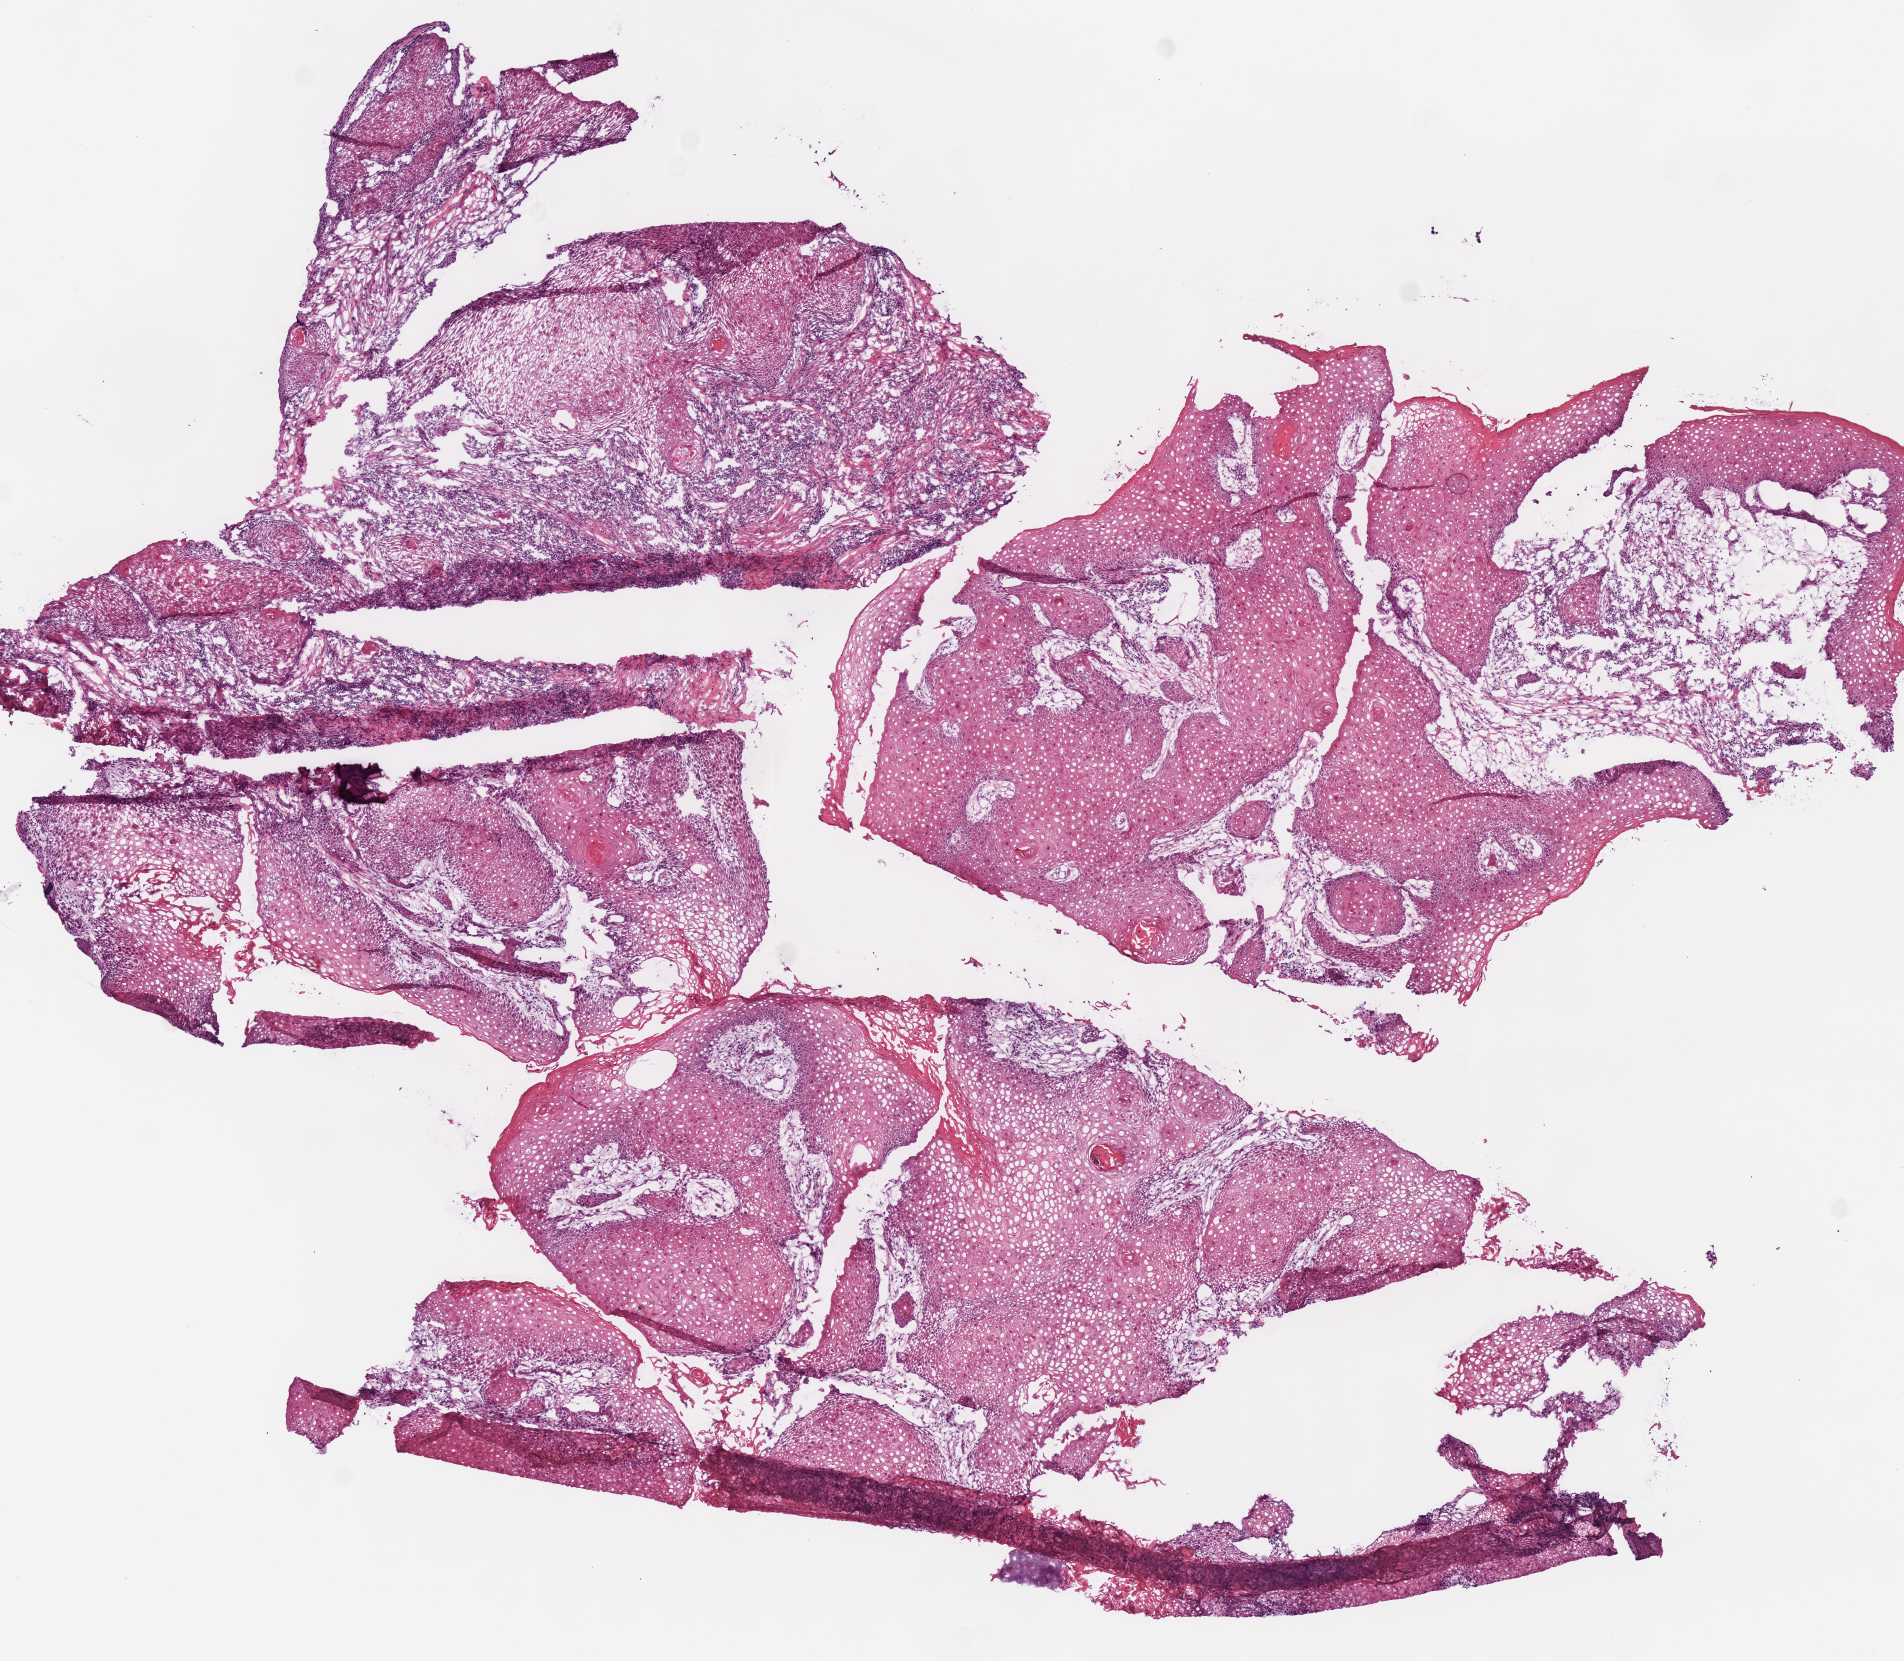
Digitized H&E-stained tissue section (whole slide), whole scanned area (about 7.5 x 6.5 mm, acquisition: 40x scan) shown as a low-resolution overview. Frozen section from the top of the tissue portion. Primary tumour sample from the head and neck. Patient: female, age at initial diagnosis 64 years. Histologic grade: G1 (well differentiated). Composition of this section per pathologist review: tumour cells 86%, tumour nuclei 71%, normal cells 0%, stromal cells 14%, necrosis 0%. Inflammatory infiltration, as recorded: lymphocyte infiltration 20%, monocyte infiltration 0%, neutrophil infiltration 0%.
* diagnosis: Squamous cell carcinoma, NOS (overlapping lesion of lip, oral cavity and pharynx)
* AJCC pathologic stage: IVA (7th edition)
* laterality: left